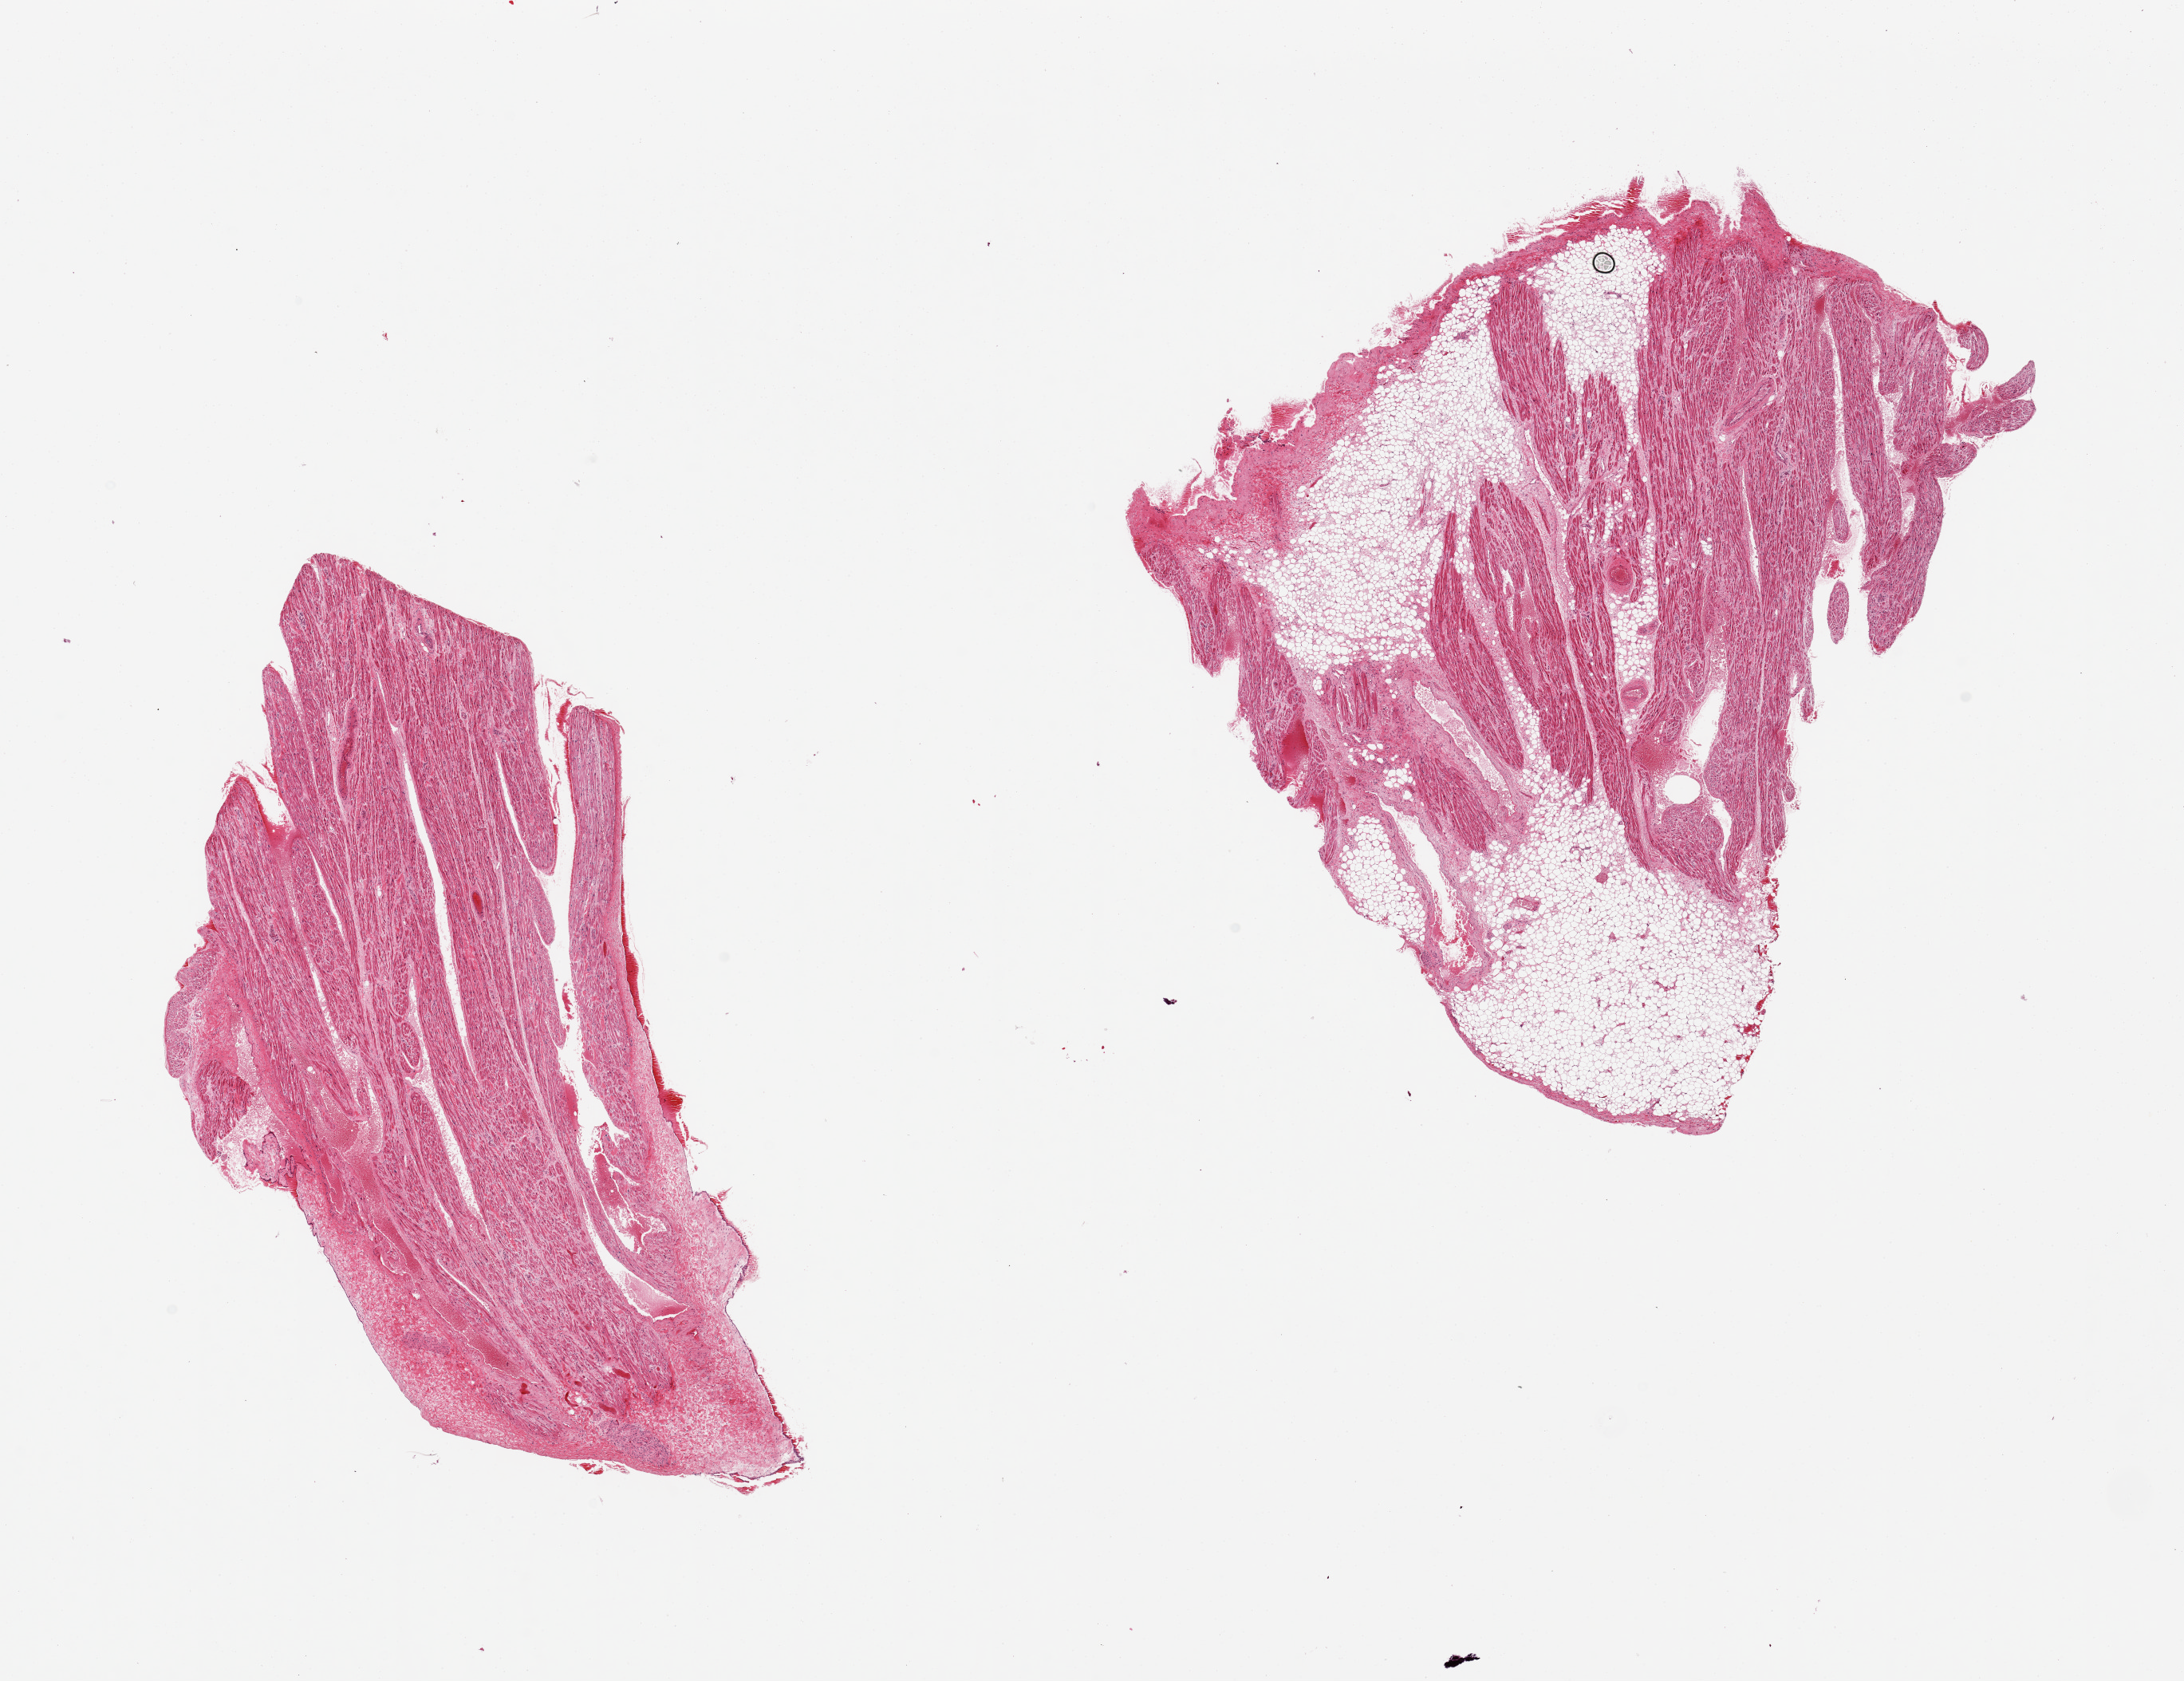
Whole-slide image, H&E stain, whole scanned area (about 21.7 x 16.7 mm) shown as a low-resolution overview. PAXgene-fixed, paraffin-embedded tissue. Target tissue: auricular appendage. Donor tissue sample.
Reviewer comment on this tissue sample: 2 pieces, one is ~40% fat.